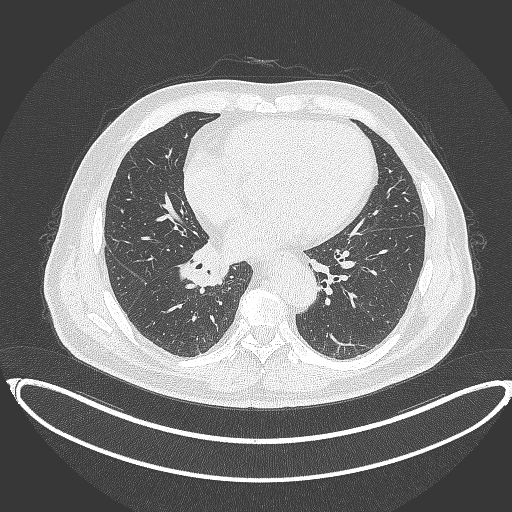
Chest CT, one axial slice; position 173 of 387 along the scan axis; reconstruction kernel B70f; lung window (W 1500 / L -600 HU); 1 mm slice thickness; 512 × 512 image matrix, field of view 448 × 448 mm. Patient: male, 61 years. From the clinical record (not read from this slice): clinical TNM (as recorded): T1b N1 M0.
Structures marked on this image (rectangle marked by the reading radiologist):
- lung tumour (recorded histology: squamous cell carcinoma): bounding box (x1, y1, x2, y2) in pixels: (172, 237, 229, 292)